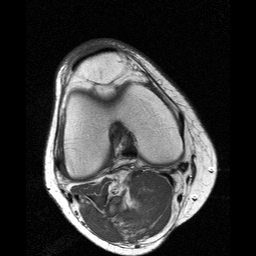
MRI of an extremity soft-tissue mass, one axial slice; slice 6 of 25 in the series (ordered by position); 256 × 256 image matrix, field of view 160 × 160 mm. Female patient. Case-level facts recorded for this patient, not image findings: histological type: liposarcoma; site of the primary tumour: right thigh.
Structures marked on this image (expert manual segmentation):
- gross tumour volume (mass): bounding box [x1, y1, x2, y2] px = [115, 208, 146, 236]